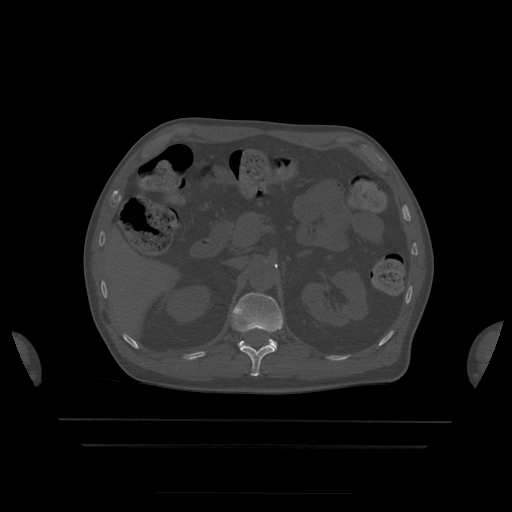
CT including the spine, one axial slice. Slice 184 of 522 in the series (ordered by position). Bone window (W 1800 / L 400 HU). 512 × 512 image matrix. Patient age 68 years. From the clinical record (not read from this slice): primary cancer: urothelial.
Outlined on this slice (semi-automatically segmented with operator editing):
- L1 vertebra: bounding box (x1, y1, x2, y2) in pixels: (232, 293, 283, 350)
- T12 vertebra: (240, 343, 276, 377)